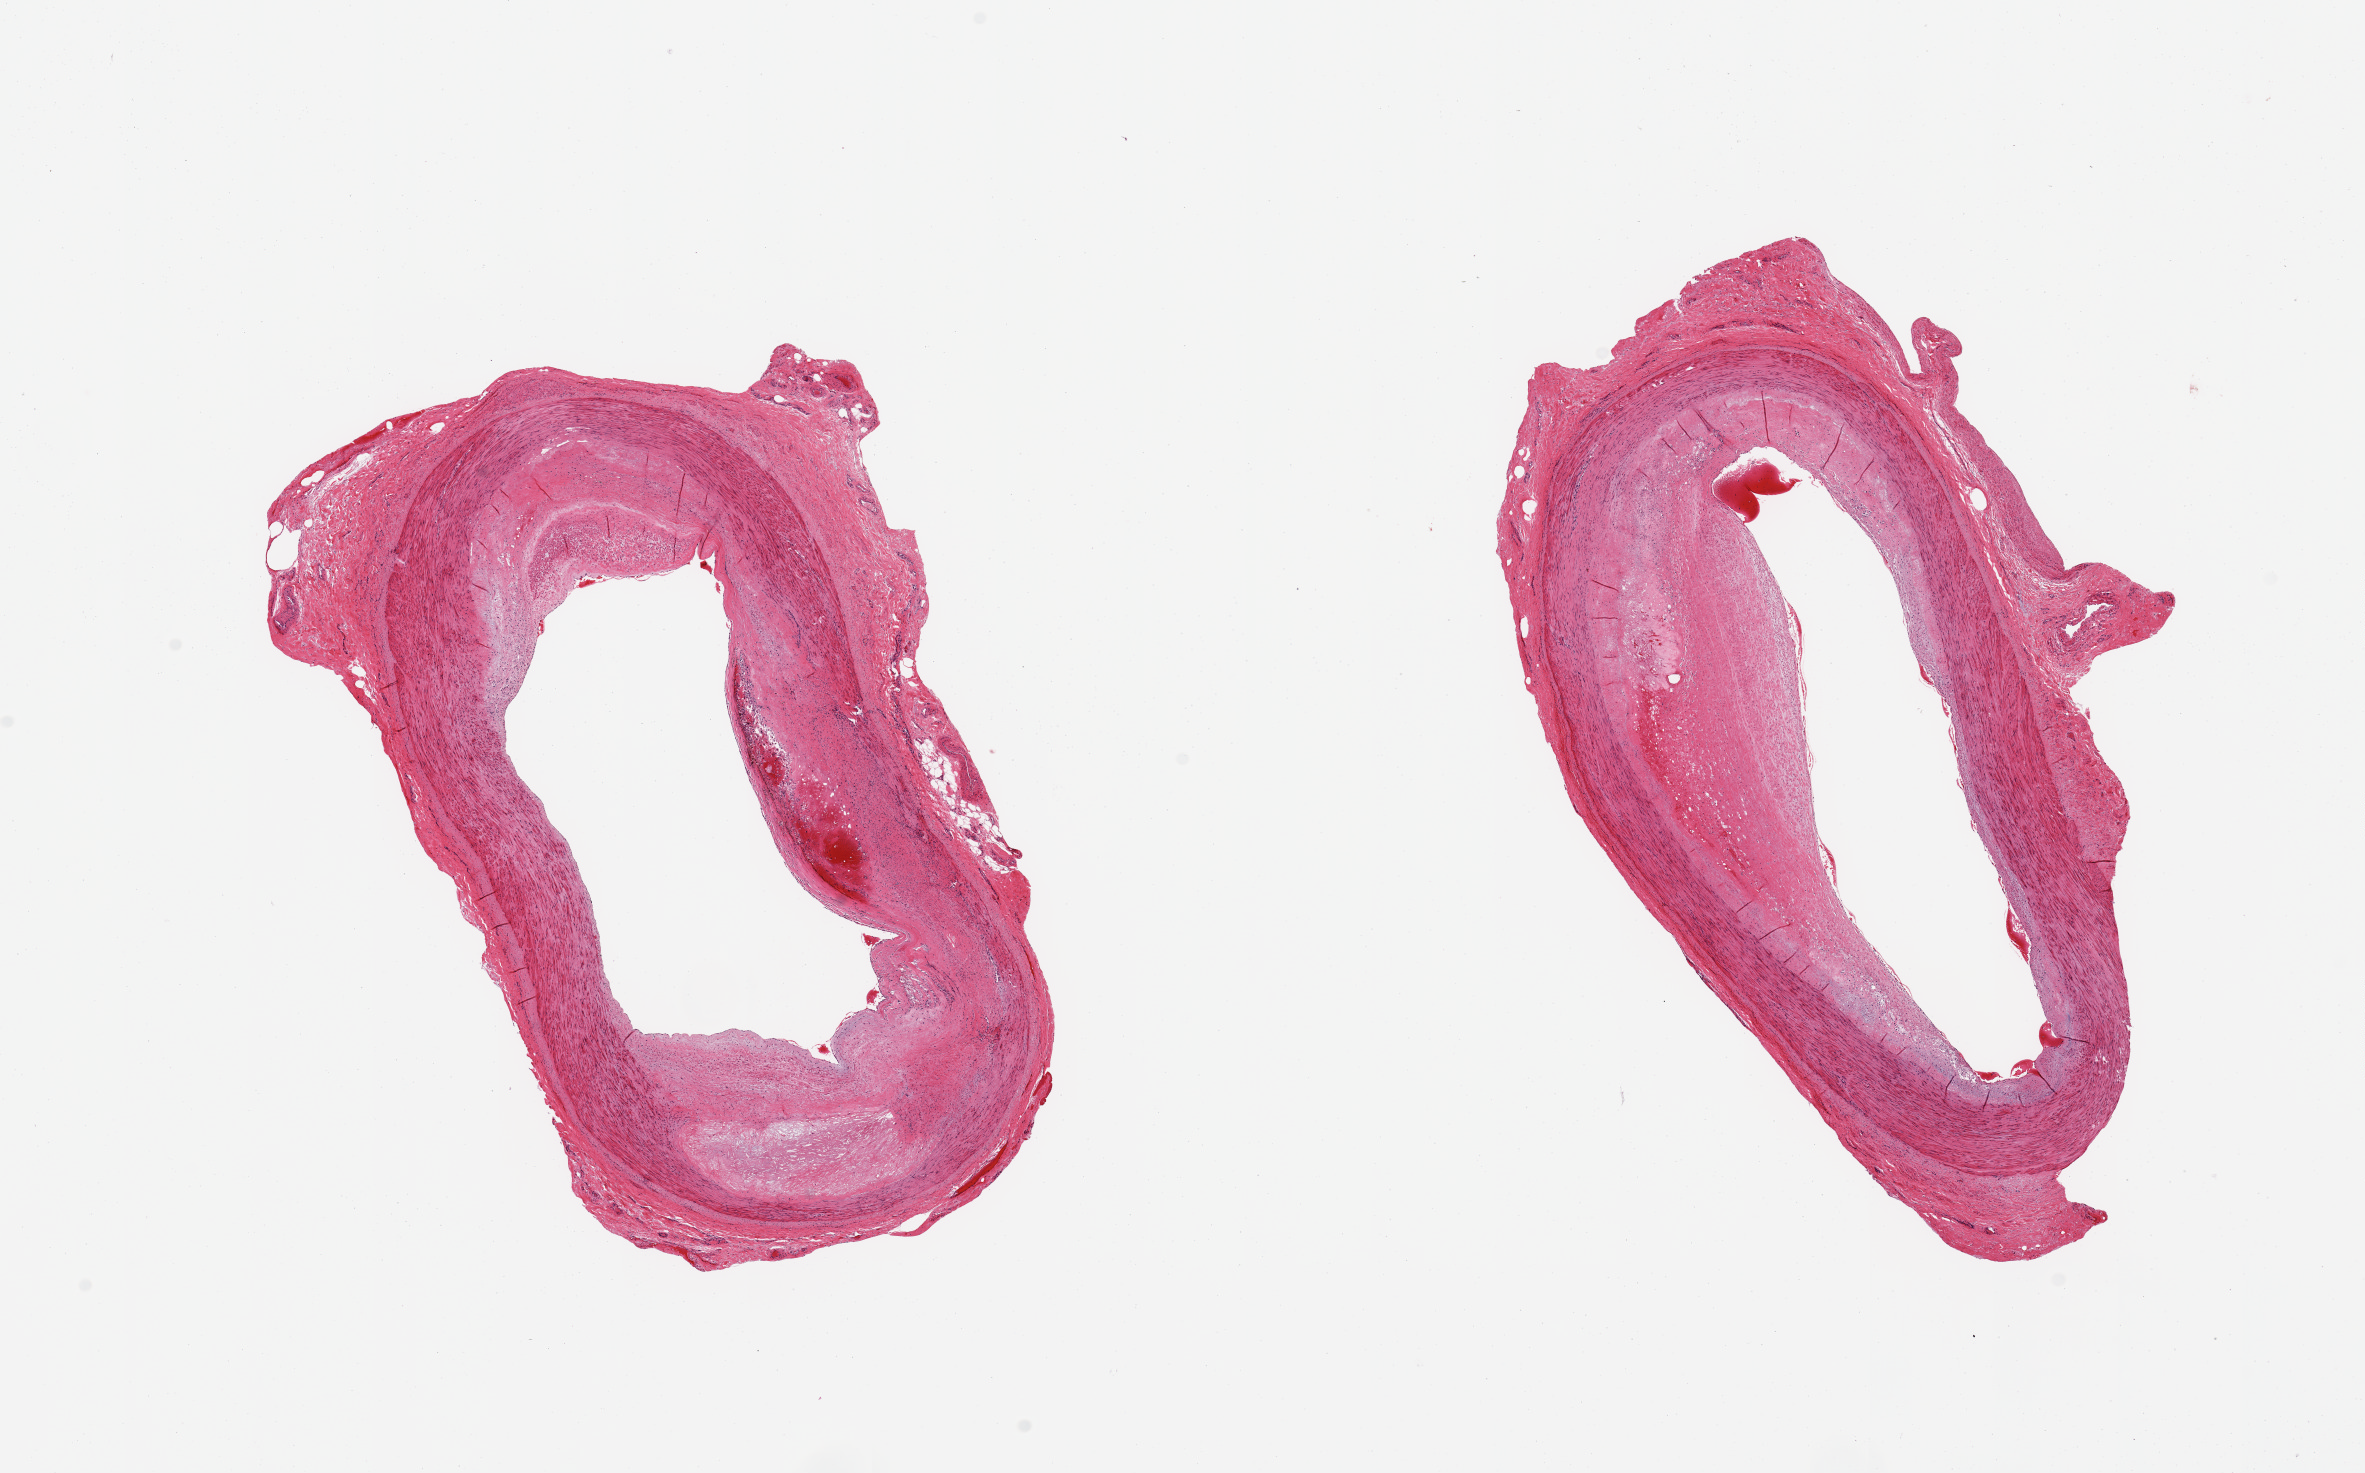
Whole-slide image, haematoxylin and eosin stain — whole scanned area (about 18.7 x 11.6 mm) shown as a low-resolution overview. PAXgene-fixed, paraffin-embedded tissue. Sampled site (target tissue): tibial artery. Donor tissue sample. Donor sex: male.
Reviewer comment on this tissue sample: 2 pieces; atheromatous plaque with mural organizing thrombosis narrowing the lumen by ~50% and 75%; ~1mm of attached adventitia.